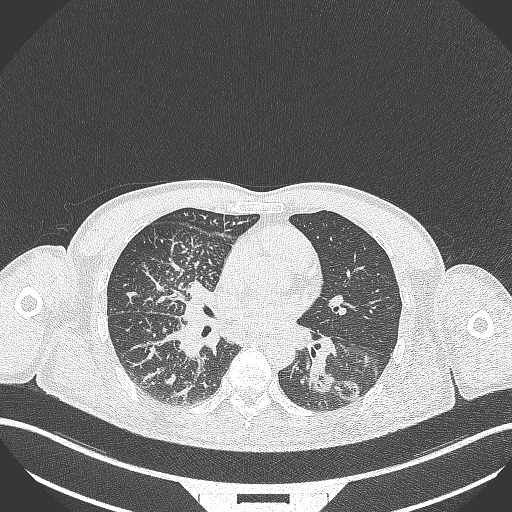
Chest CT, one axial slice; position 156 of 348 along the scan axis; 120 kVp; lung window (W 1500 / L -600 HU); 512 × 512 image matrix, field of view 400 × 400 mm. Patient: male, 49 years. Case-level facts recorded for this patient, not image findings: clinical TNM (as recorded): T2b N1 M0.
Outlined on this slice (rectangle marked by the reading radiologist):
- lung tumour (recorded histology: adenocarcinoma): bounding box <308,361,365,404> (left, top, right, bottom; pixels)